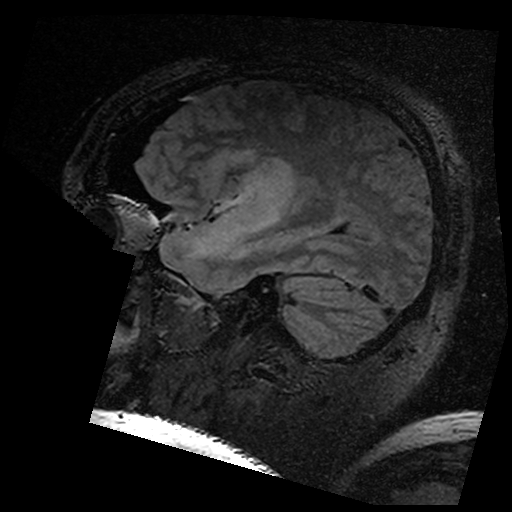
Brain MRI from a brain-tumour surgery series, one sagittal slice. T2 FLAIR. 1 mm slice thickness. 512 × 512 image matrix, field of view 250 × 250 mm. Case-level facts recorded for this patient, not image findings: histopathology: Astrocytoma; WHO grade: 3; IDH mutation: yes; tumour location: Left Insular.
Annotated regions visible in this slice (outlined manually by an expert reader):
- residual tumour: bounding box [x1, y1, x2, y2] px = [211, 146, 293, 201]